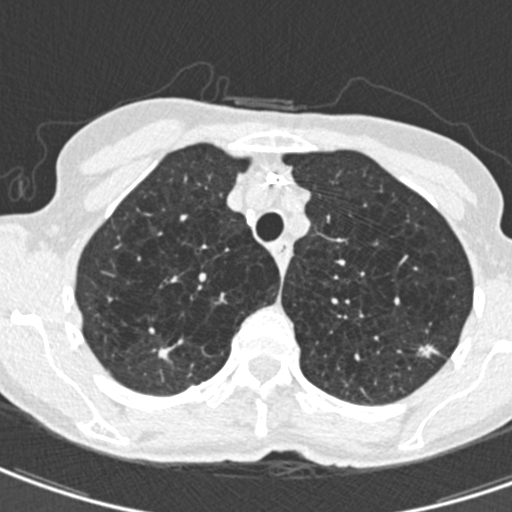
Low-dose screening chest CT, axial slice; second annual screen; lung window (W 1500 / L -600 HU); 0.75 mm slice thickness; standard (soft-tissue) reconstruction kernel (B30f); slice 116 of 498 in the series. Female participant, aged 71 years at enrolment.
• Lesion marked by an expert reader, bounding box (x1, y1, x2, y2) in pixels: (404, 331, 444, 369).
• The screening reader recorded 2 non-calcified nodules or masses ≥4 mm on this exam (right upper lobe, left upper lobe); which of them this box marks is not recorded.
• Later outcome: lung cancer diagnosed 604 days after this screen (after the third annual screen) — adenocarcinoma, NOS, left upper lobe, moderately differentiated (G2), stage IA (AJCC 6th edition), 12 mm at pathology.